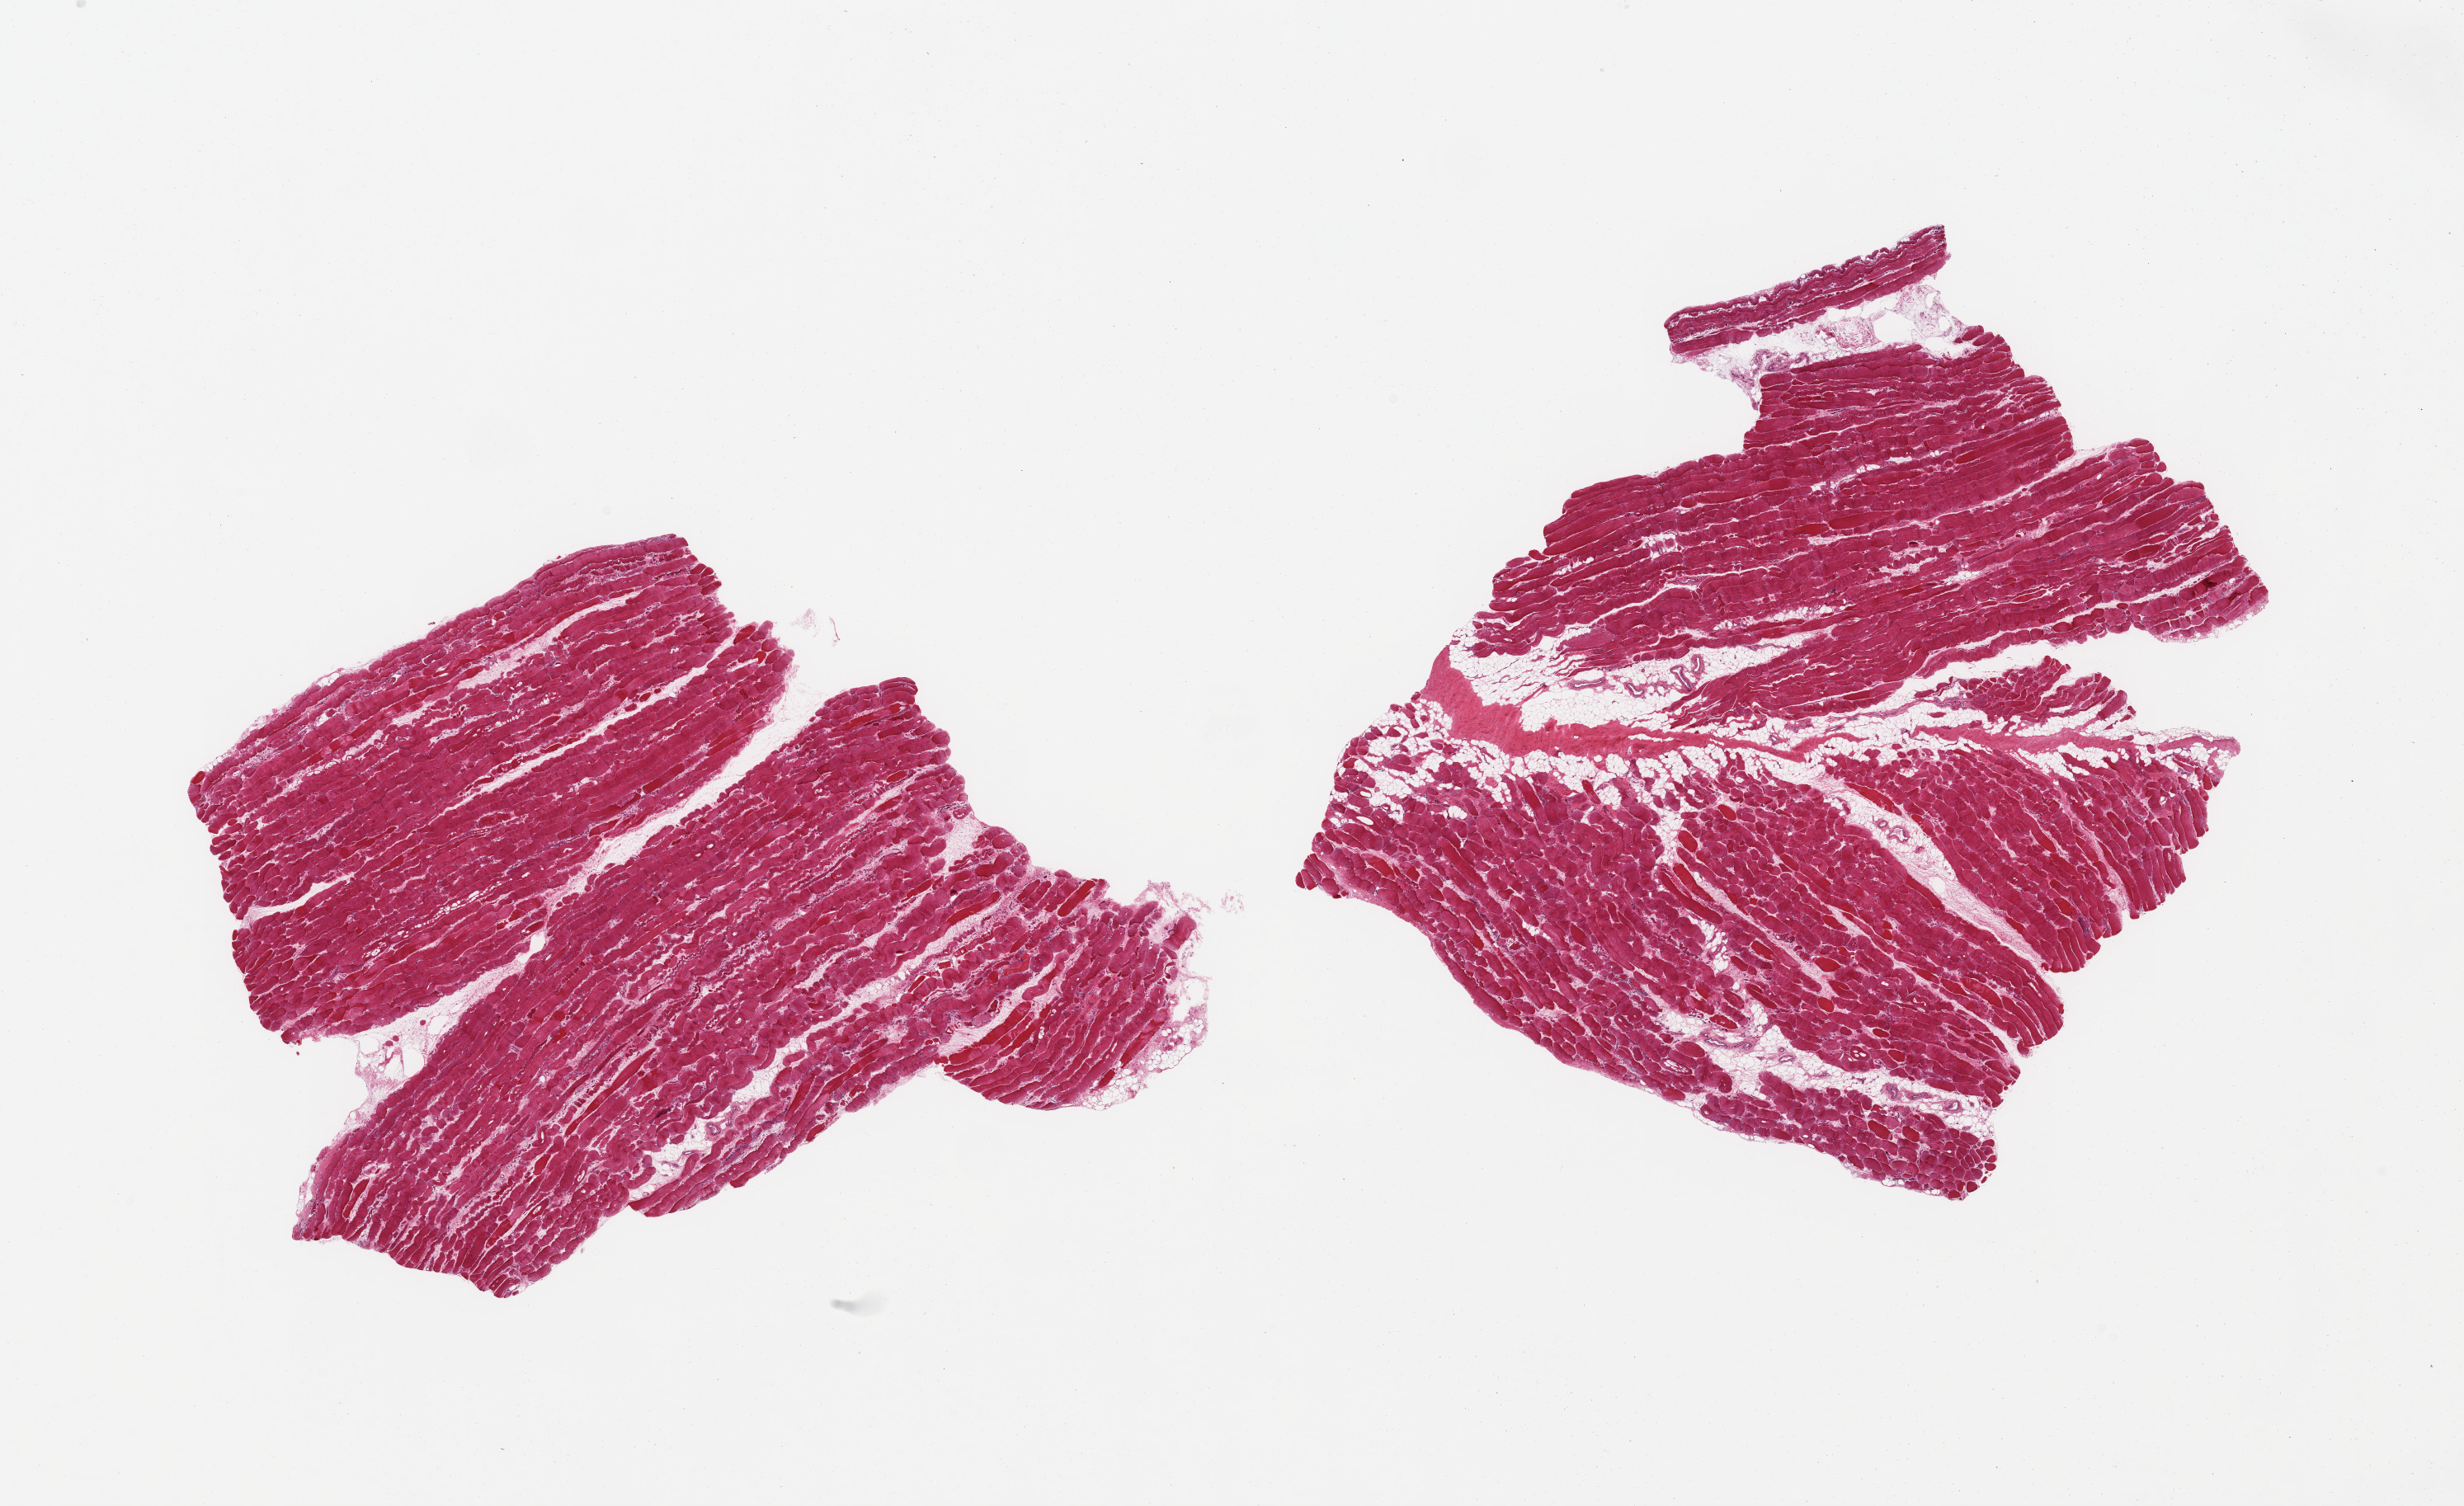
Hematoxylin and eosin (H&E) whole-slide image — a low-resolution overview of the entire scanned area, about 23.6 x 14.4 mm; PAXgene-fixed, paraffin-embedded tissue; sampled site (target tissue): skeletal muscle; tissue donor sample.
Reviewer comment on this tissue sample: 2 pieces; one piece contains ~10% internal fat.